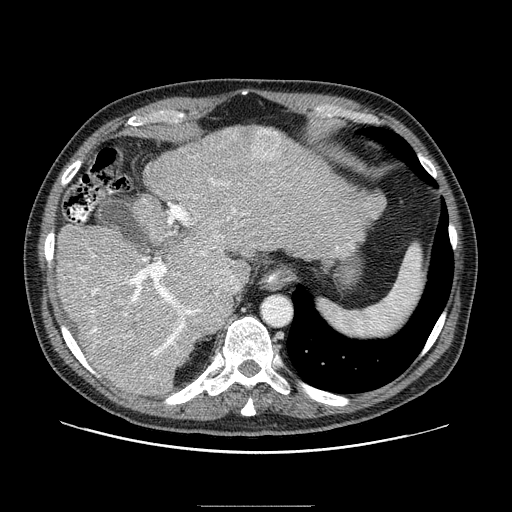
Contrast-enhanced abdominal CT (liver protocol), one axial slice. Slice 64 of 99 in the series (ordered by position). Reconstruction kernel STANDARD. 100 kVp. One of 2 acquisitions stored at this slice position. Soft-tissue window (W 400 / L 40 HU). 2.5 mm slice thickness. 512 × 512 image matrix, field of view 400 × 400 mm. From the clinical record (not read from this slice): diagnosis: hepatocellular carcinoma (patient treated with transarterial chemoembolisation; whether this scan precedes or follows treatment is not stated here); TNM stage (as recorded): Stage-II; Child-Pugh class: A; tumour nodularity: multinodular; tumour size: 3.2 cm.
Outlined on this slice (semi-automatic segmentation, software-assisted and operator-edited):
- abdominal aorta: bounding box (x1, y1, x2, y2) in pixels: (263, 297, 291, 324)
- liver parenchyma outside the tumour (the mass and vessels are separate outlines, so this box may not span the whole liver): (56, 126, 385, 394)
- mass: (250, 127, 283, 162)
- liver vessels: (64, 170, 339, 379)